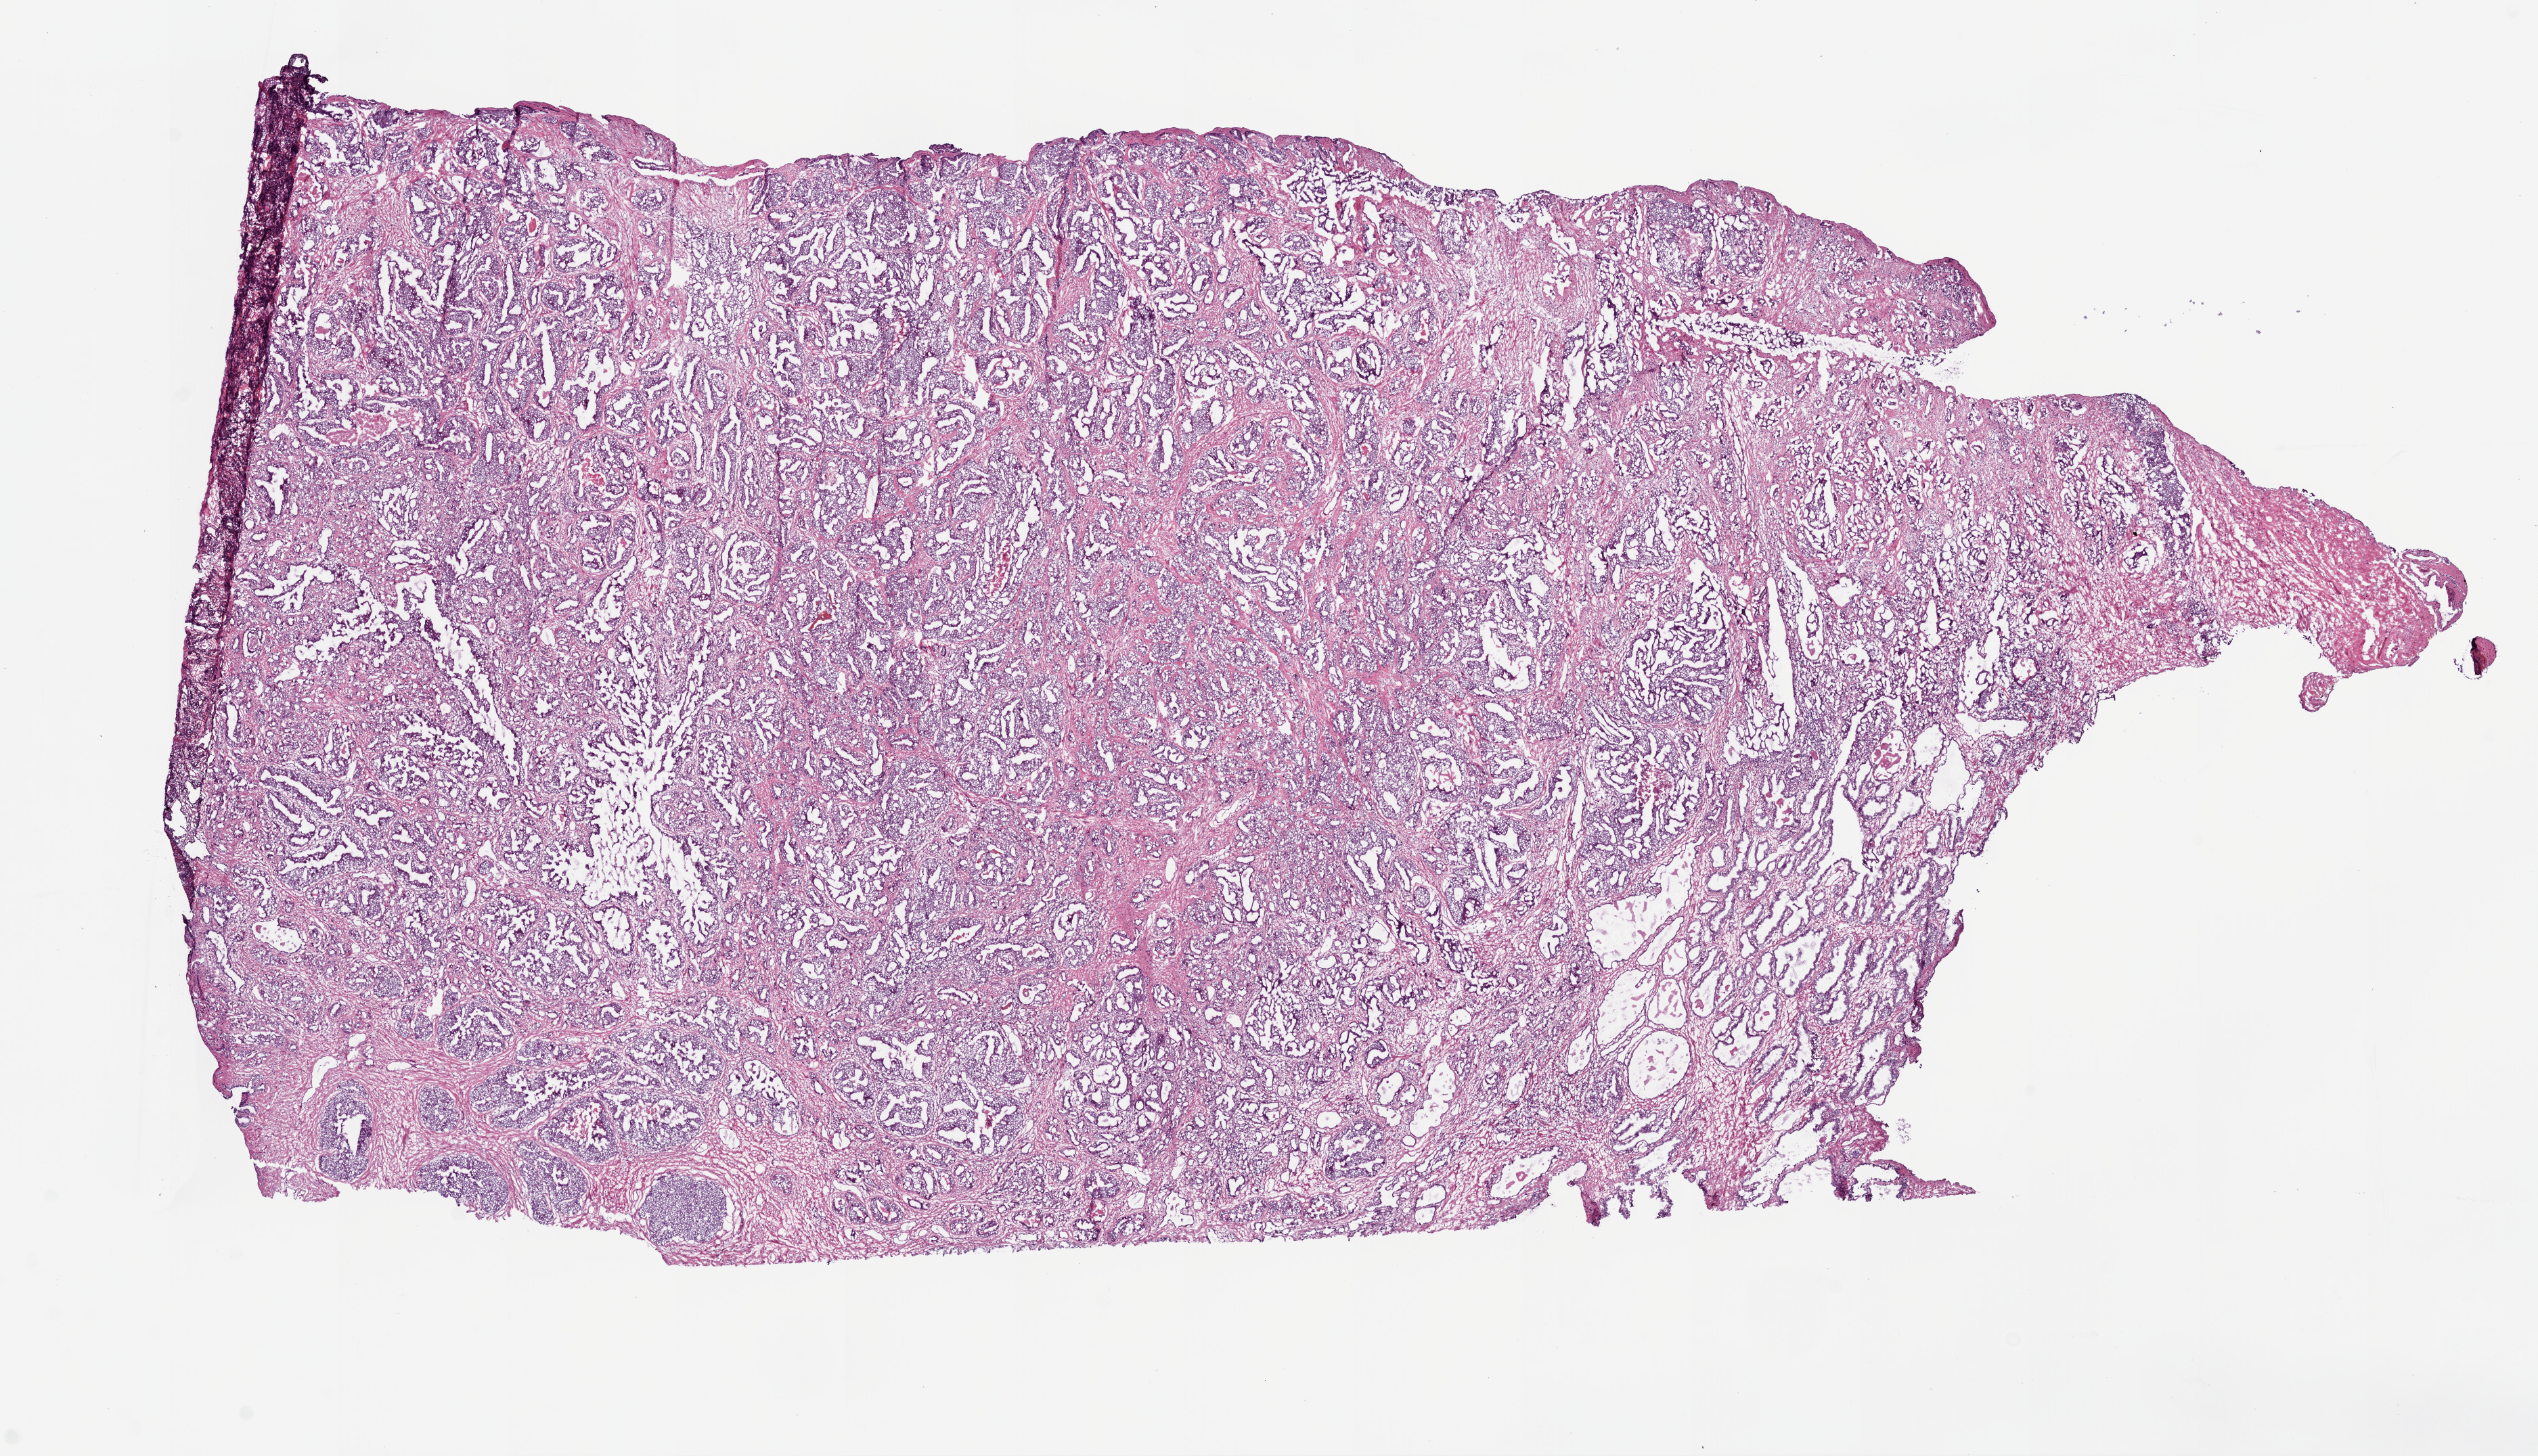
H&E-stained whole-slide image, low-resolution overview of the scanned area, about 15.0 x 8.6 mm (from a 20x scan). Frozen section from the top of the tissue portion. Primary tumour sample from the prostate. Patient: male, age at initial diagnosis 54 years. Composition of this section per pathologist review: tumour cells 55%, tumour nuclei 60%.
Histologic diagnosis: Acinar cell carcinoma (prostate gland).